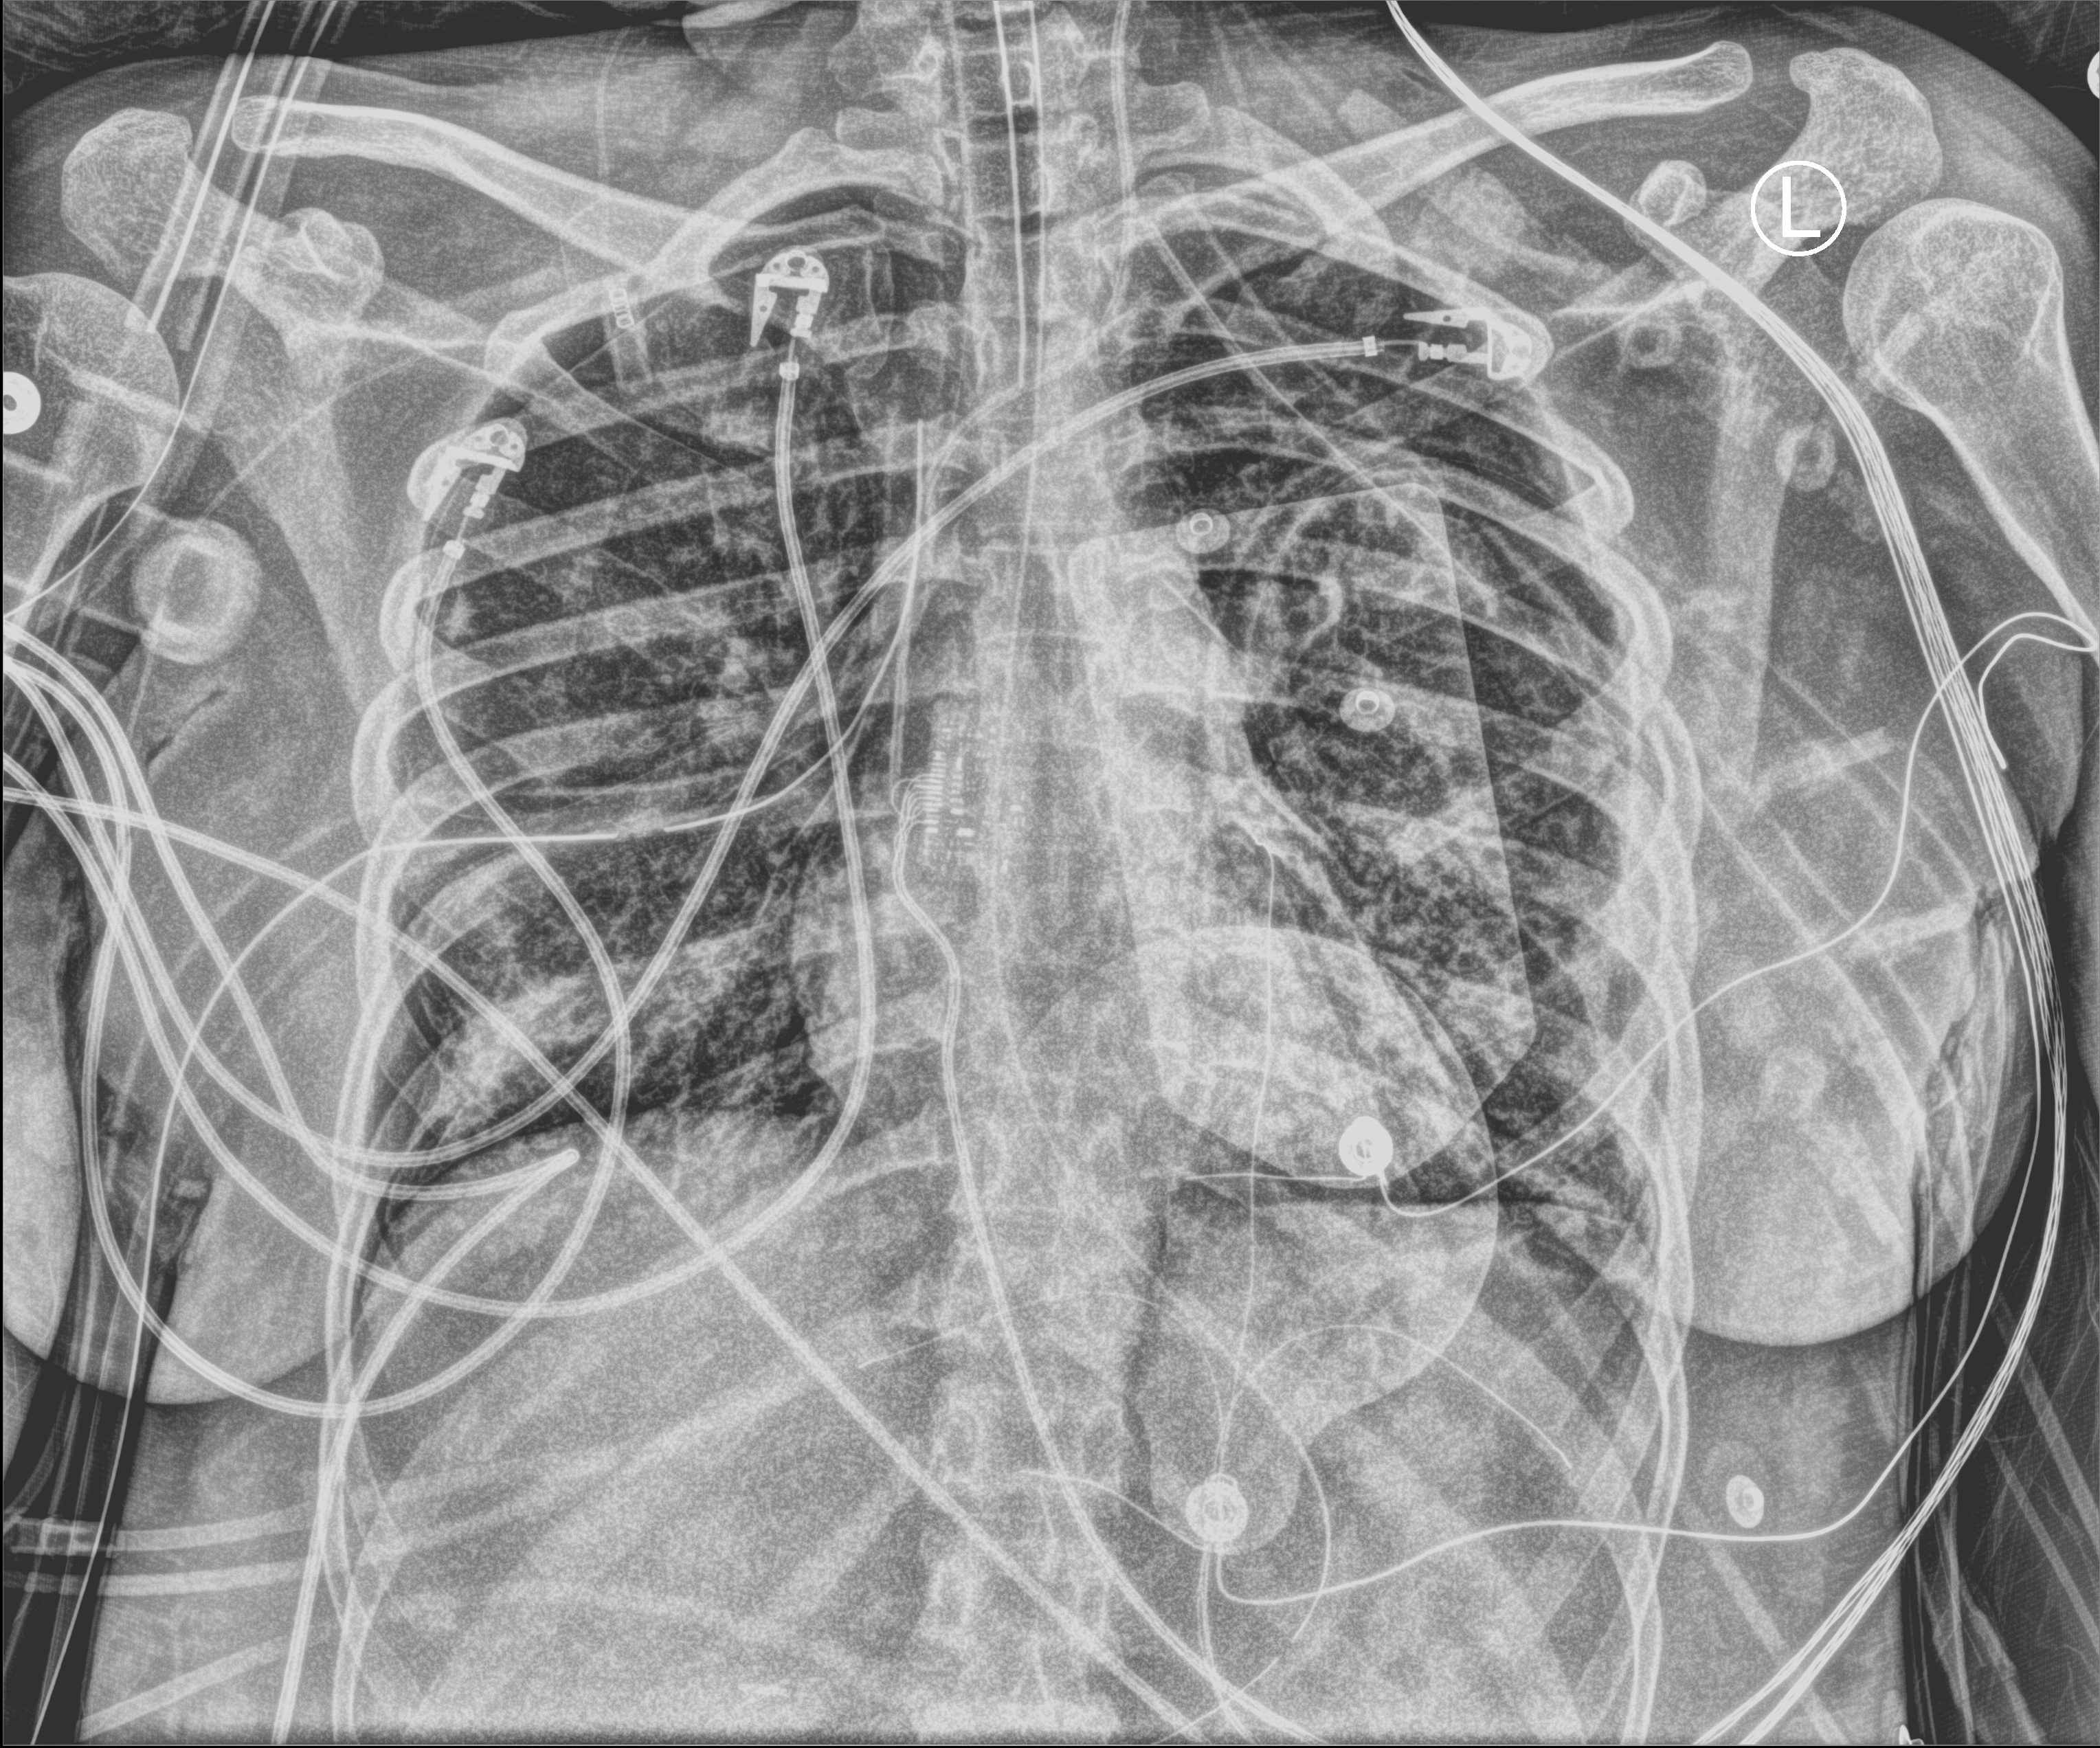
Portable chest radiograph; anteroposterior (AP) projection. Adult patient hospitalised with COVID-19, age 18–59 years.
Admission-level facts for this patient (not findings on this image; timing relative to this image not recorded): admitted to intensive care during this hospital stay: yes.